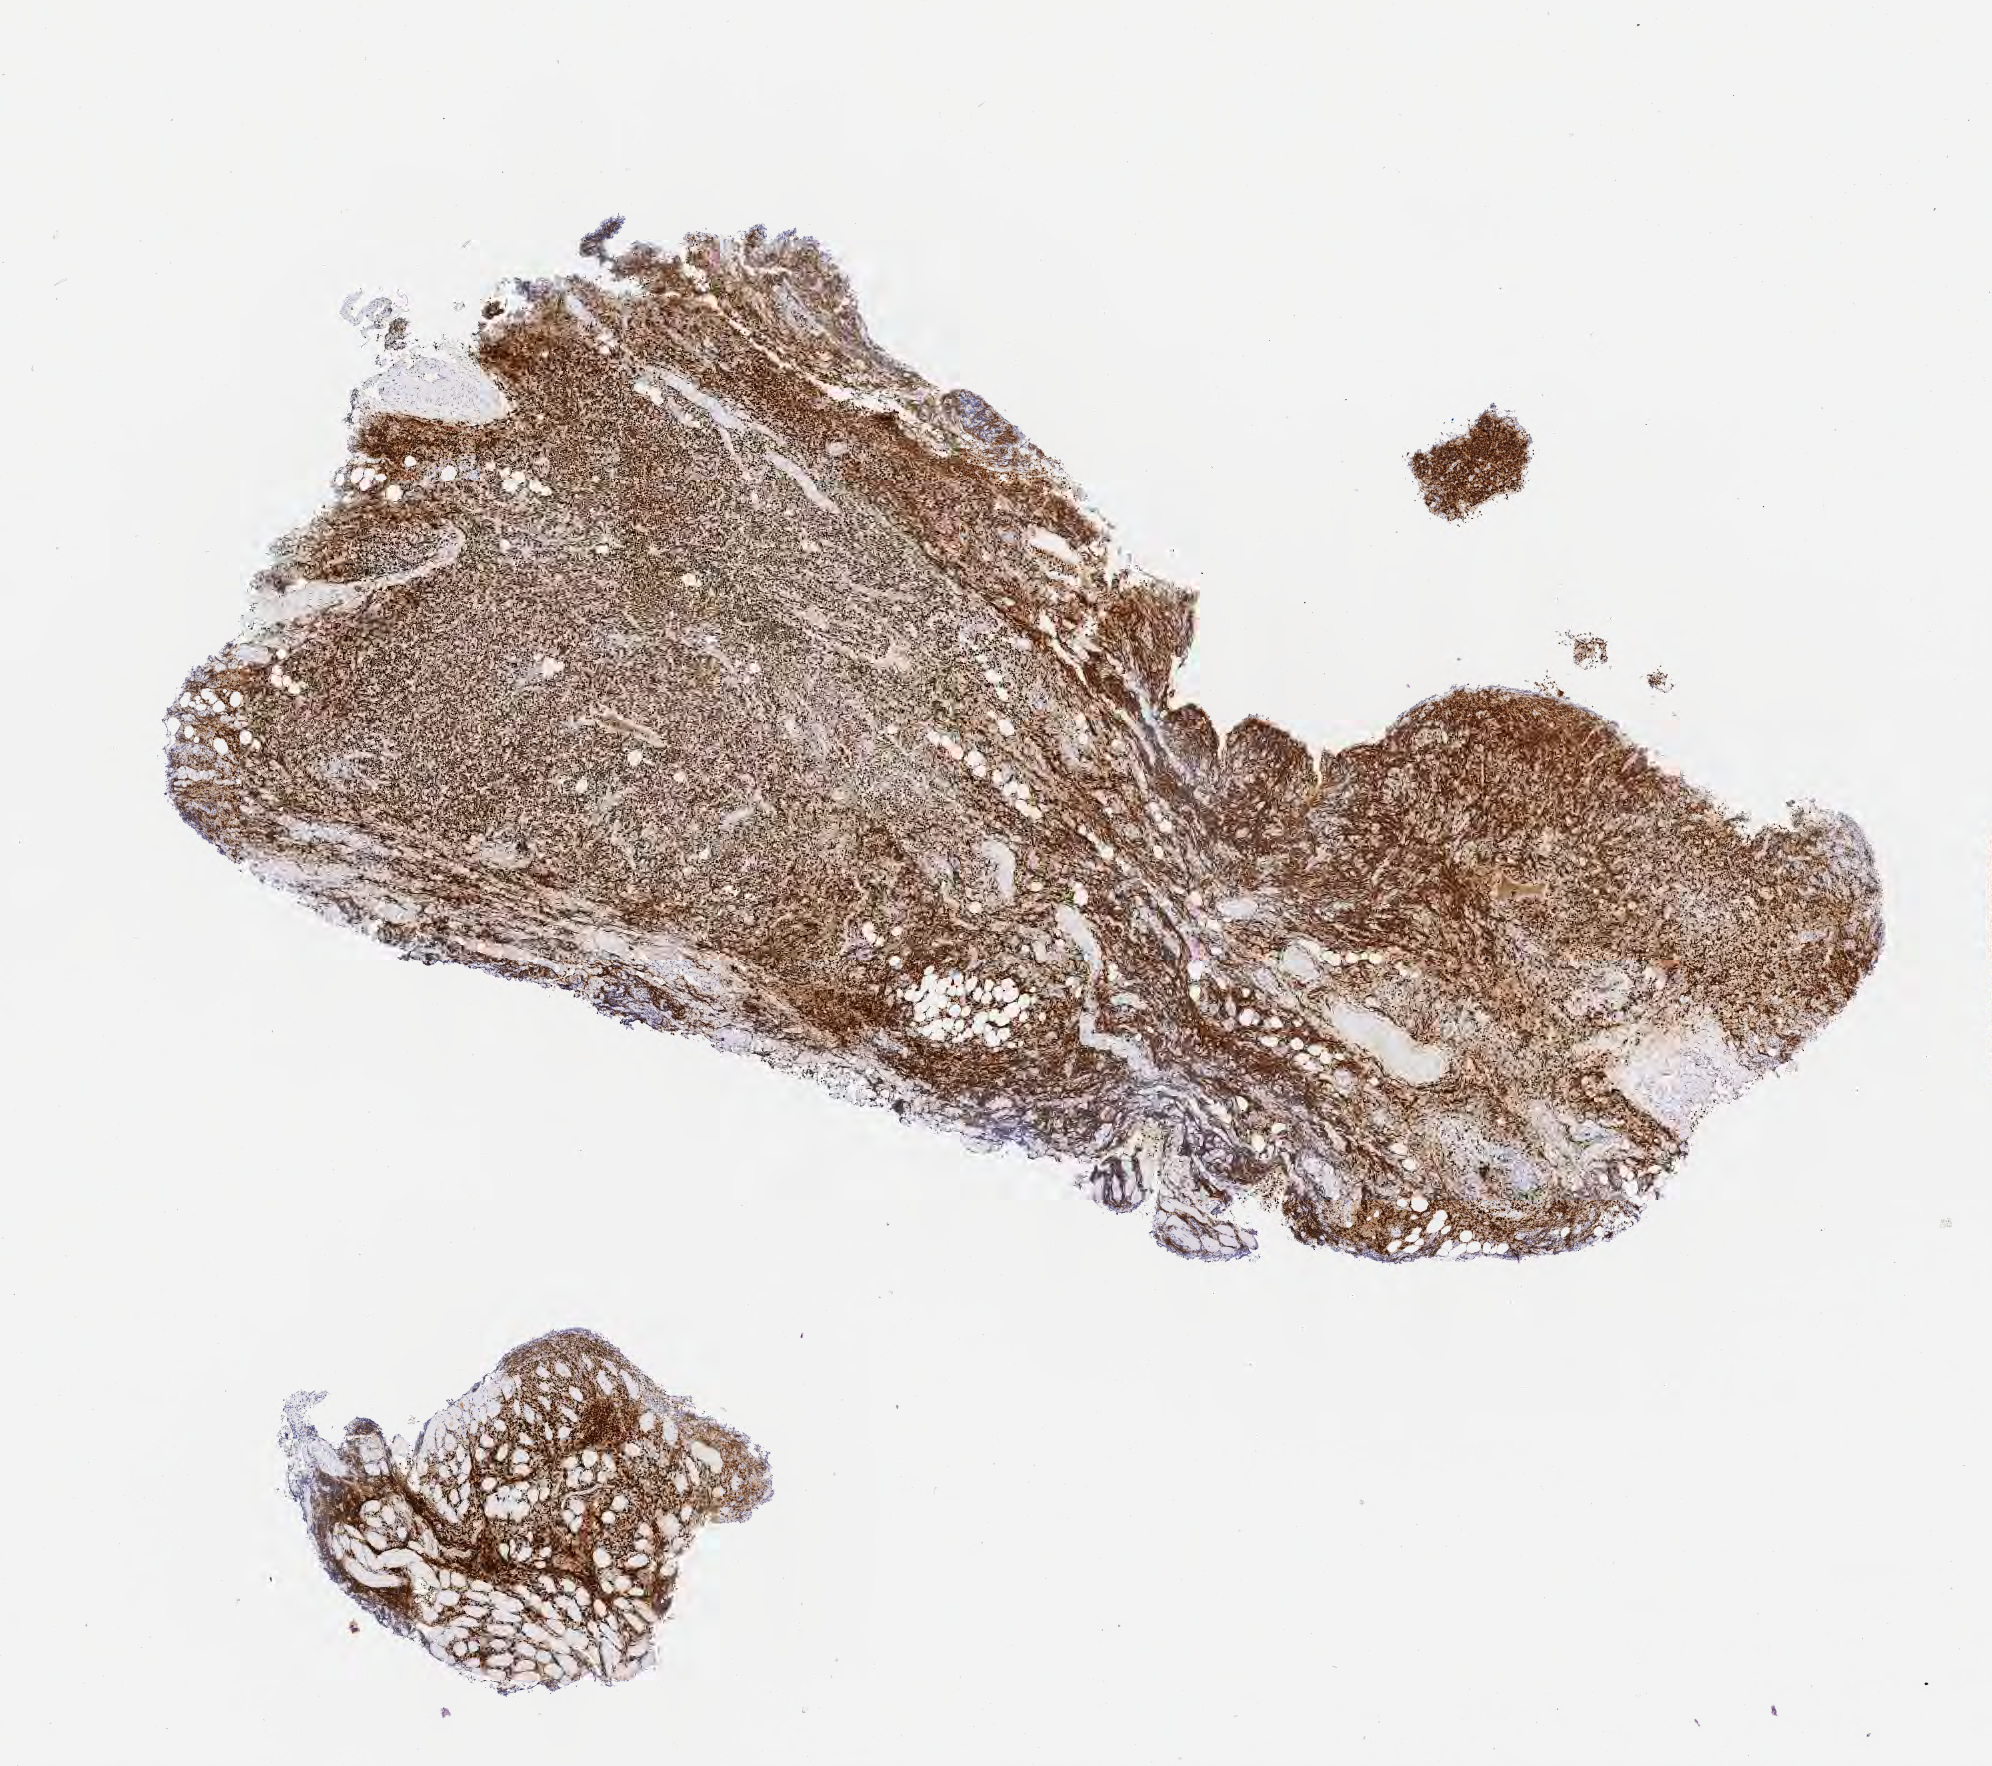
Immunohistochemistry (IHC) whole-slide image stained for IRF4/MUM1, a low-resolution overview of the entire scanned area, about 8.0 x 7.1 mm; specimen: tumor tissue. Patient male; aged 67.
• histologic diagnosis: Diffuse large B-cell lymphoma, NOS